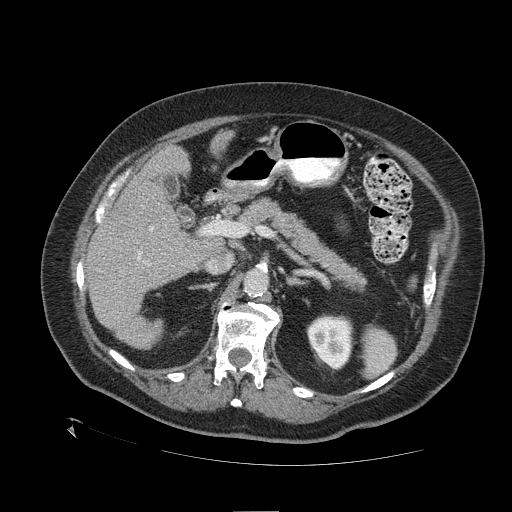
Contrast-enhanced abdominal CT (liver protocol), one axial slice. Position 63 of 109 along the scan axis. Reconstruction kernel STANDARD. One of 2 acquisitions stored at this slice position. Soft-tissue window (W 400 / L 40 HU). 2.5 mm slice thickness. 512 × 512 image matrix. Case-level facts recorded for this patient, not image findings: diagnosis: hepatocellular carcinoma (patient treated with transarterial chemoembolisation; whether this scan precedes or follows treatment is not stated here); TNM stage (as recorded): Stage-I; Child-Pugh class: A.
Outlined on this slice (semi-automatically segmented with operator editing):
- liver parenchyma outside the tumour (the mass and vessels are separate outlines, so this box may not span the whole liver): bounding box (x1, y1, x2, y2) in pixels: (86, 131, 232, 348)
- liver vessels: (138, 227, 153, 264)